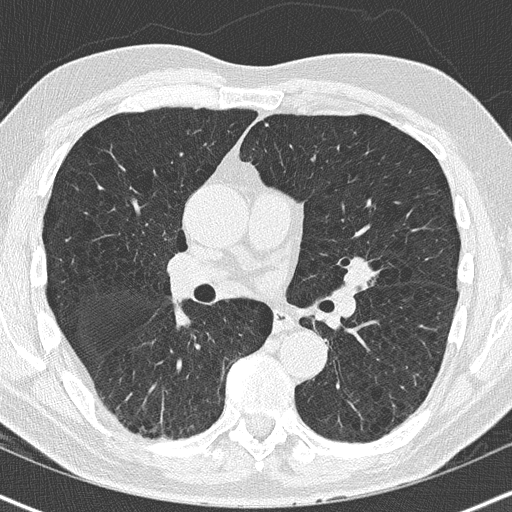
Chest CT (low-dose screening protocol), one axial image. First (baseline) screen. Lung window (W 1500 / L -600 HU). Lung (sharp) reconstruction kernel (B50f). Slice 79 of 163 in the series. 512 × 512 image matrix, field of view 320 × 320 mm. Male, age 63 years at enrolment.
Lesion marked by an expert reader, bounding box <335,255,382,293> (left, top, right, bottom; pixels). The screening reader recorded 2 non-calcified nodules or masses ≥4 mm on this exam; which of them this box marks is not recorded. Later outcome: lung cancer diagnosed 32 days after this screen — squamous cell carcinoma, NOS, left upper lobe, moderately differentiated (G2), stage IA (AJCC 6th edition), 23 mm at pathology.